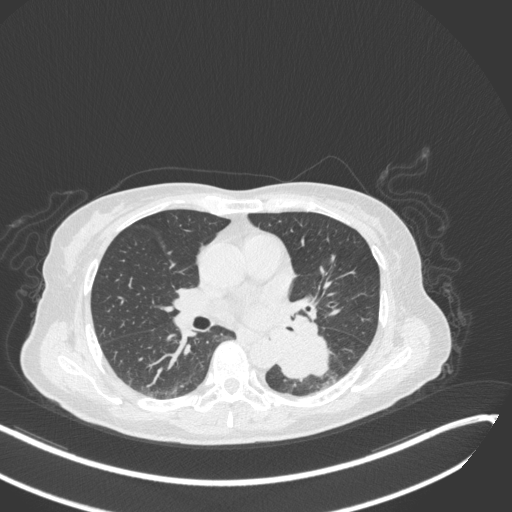
Chest CT, one axial slice. Slice 145 of 342 in the series (ordered by position). Reconstruction kernel B31f. Lung window (W 1500 / L -600 HU). 1 mm slice thickness. 512 × 512 image matrix. Patient: female, 64 years. From the clinical record (not read from this slice): clinical TNM (as recorded): T3 N1 M1.
Structures marked on this image (rectangle marked by the reading radiologist):
- lung tumour (recorded histology: small cell carcinoma): bounding box [x1, y1, x2, y2] px = [274, 332, 333, 382]